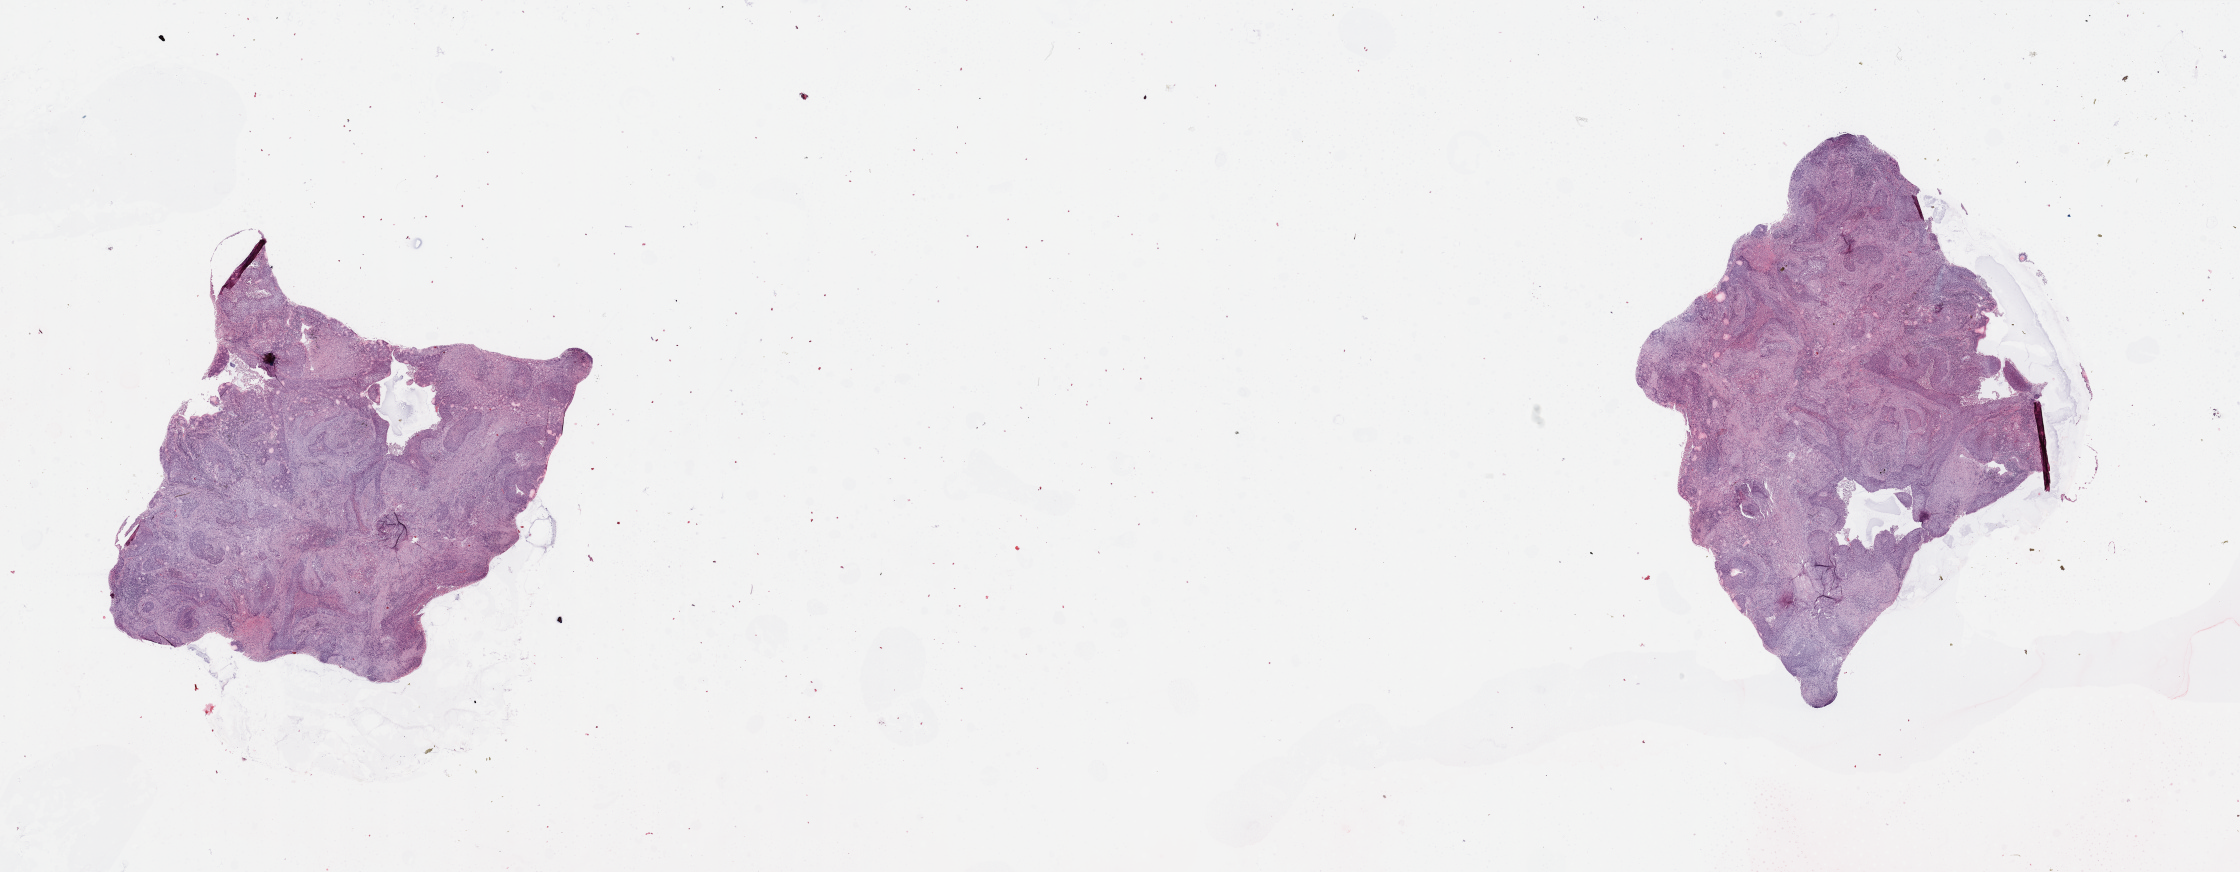
Digitized H&E-stained tissue section (whole slide) — shown as a low-resolution overview of the whole scanned area (about 35.4 x 13.8 mm, slide scanned at 20x). Lung, tumour tissue. Patient: male, age 70 years.
Diagnosis: Squamous cell carcinoma, NOS.